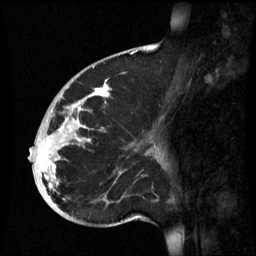
Breast MRI (dynamic contrast-enhanced), one sagittal slice. Slice 26 of 60 in the series (ordered by position). Dynamic contrast-enhanced series, image 2 of 3 at this slice position (ordered by acquisition). 1.5 T. TE 4.2 ms, TR 8.9 ms. 2.6 mm slice thickness. 256 × 256 image matrix, field of view 220 × 220 mm. Female patient, age 35 years. Case-level facts recorded for this patient, not image findings: setting: breast cancer imaged before/during neoadjuvant chemotherapy; receptor status: HR-positive, HER2-negative.
Structures marked on this image (semi-automatically segmented with operator editing):
- analysis volume of interest (the breast-tissue region the enhancement analysis was run in; not a lesion): bounding box (x1, y1, x2, y2) in pixels: (32, 74, 164, 221)
- tumour enhancement mask (voxels above the 70 % enhancement threshold inside the analysis volume of interest): (37, 80, 109, 189)